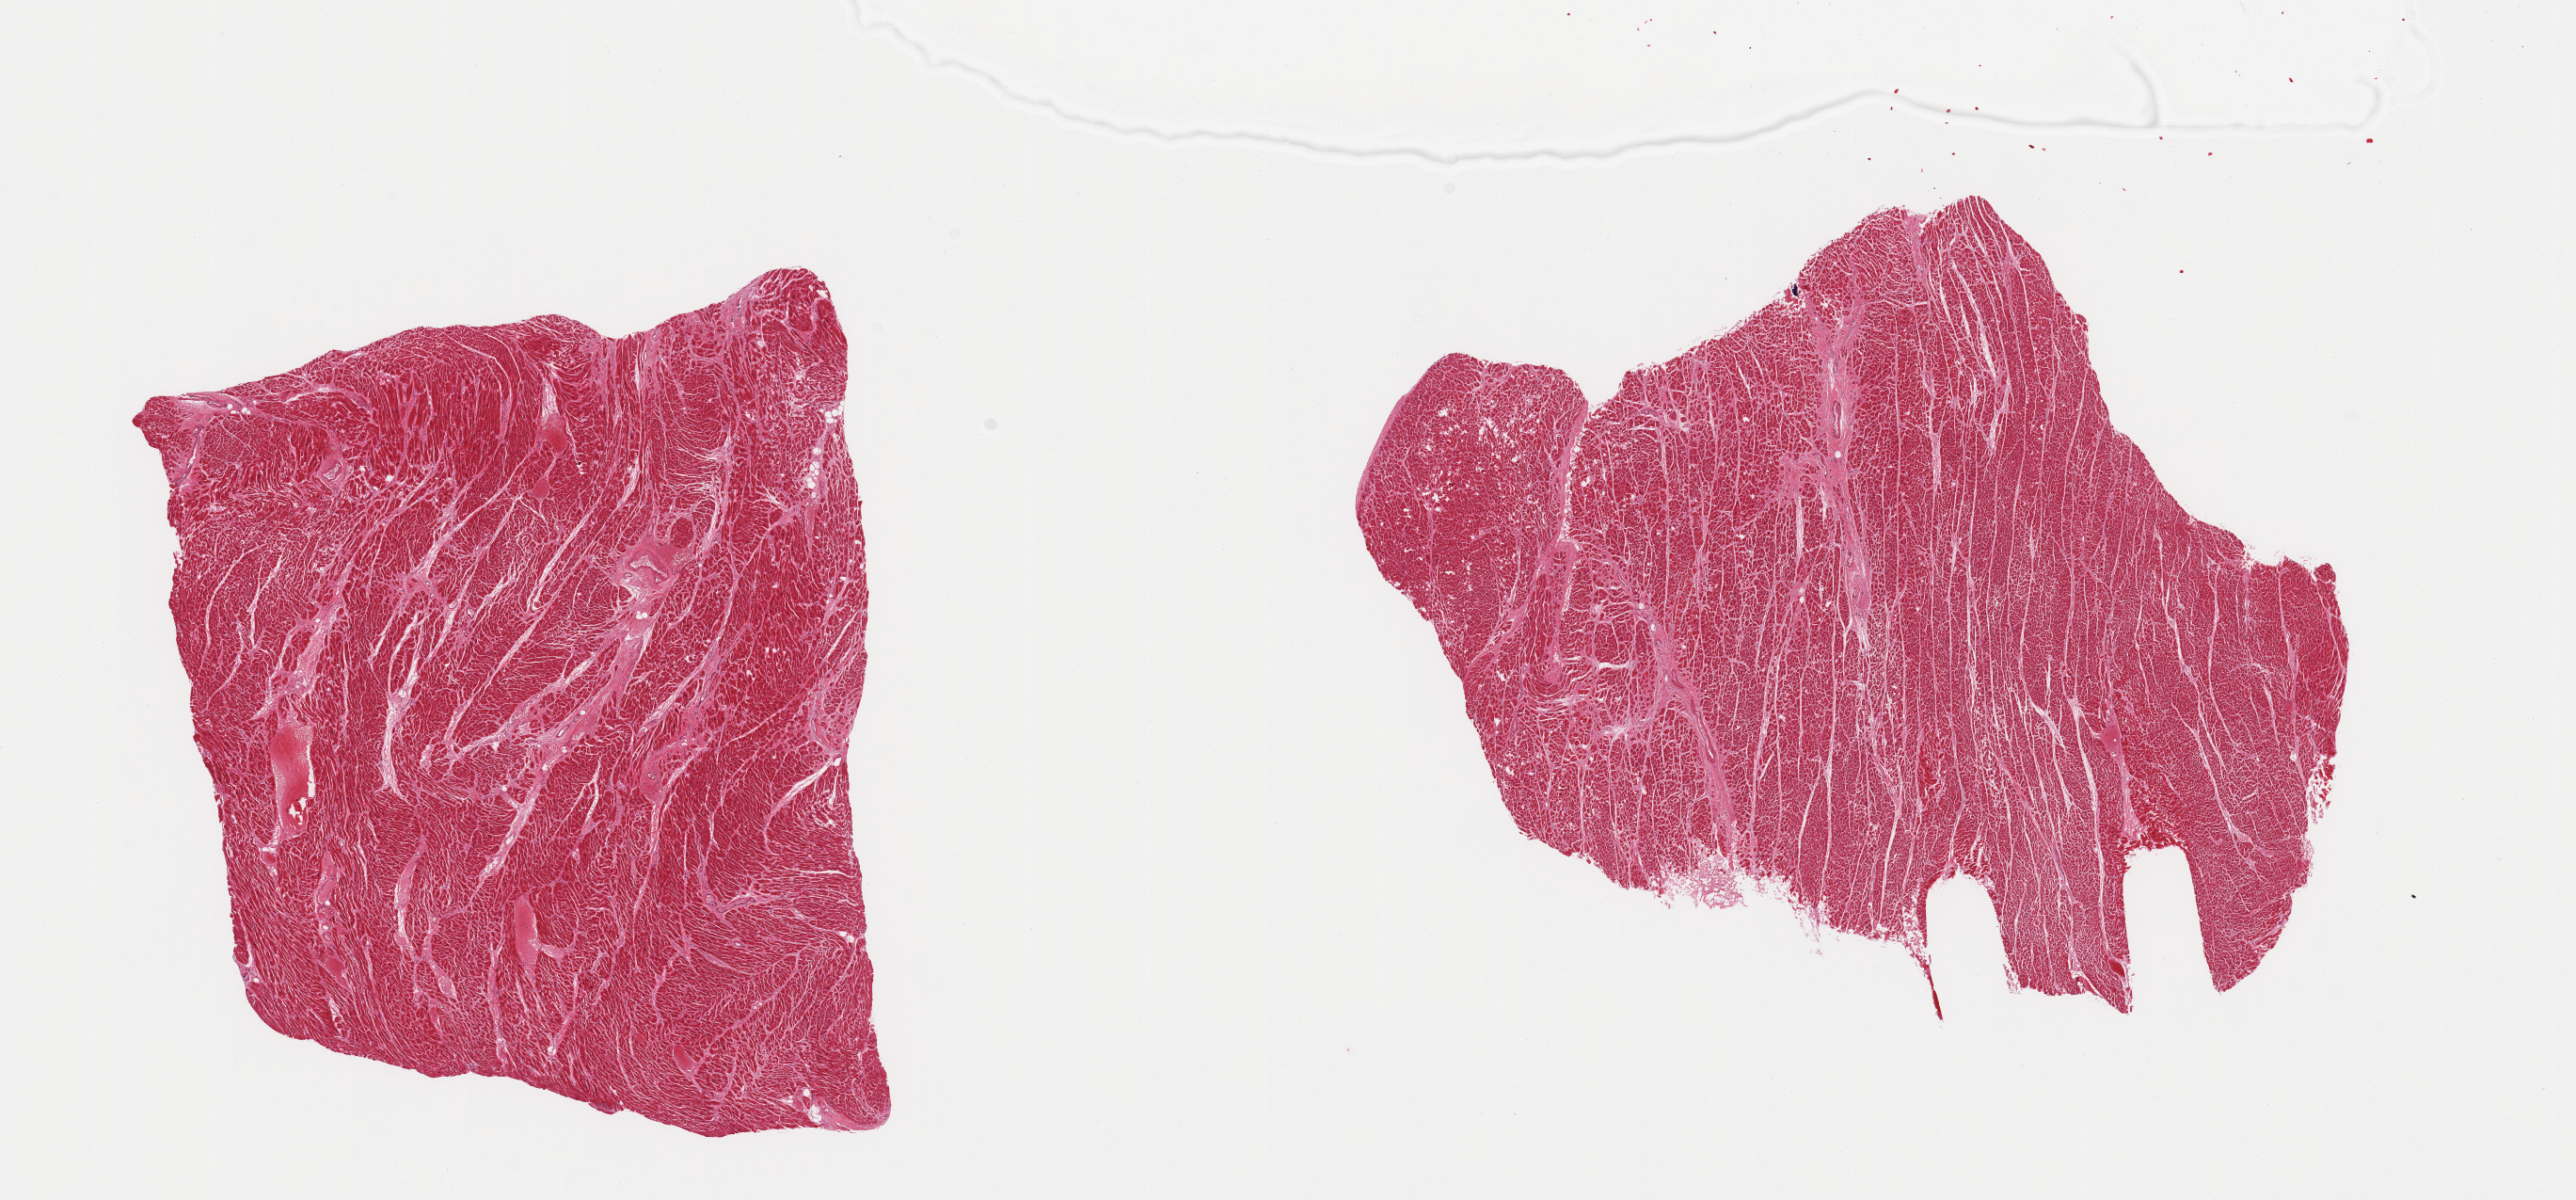
Whole-slide image, hematoxylin and eosin (H&E) stain — low-resolution overview of the scanned area, about 21.7 x 10.1 mm; PAXgene-fixed, paraffin-embedded tissue; section of heart (target tissue); tissue donor sample. Male donor.
* reviewer comment on this tissue sample: 2 pieces, moderate ischemic changes/fibrosis, microinfarct(remote)